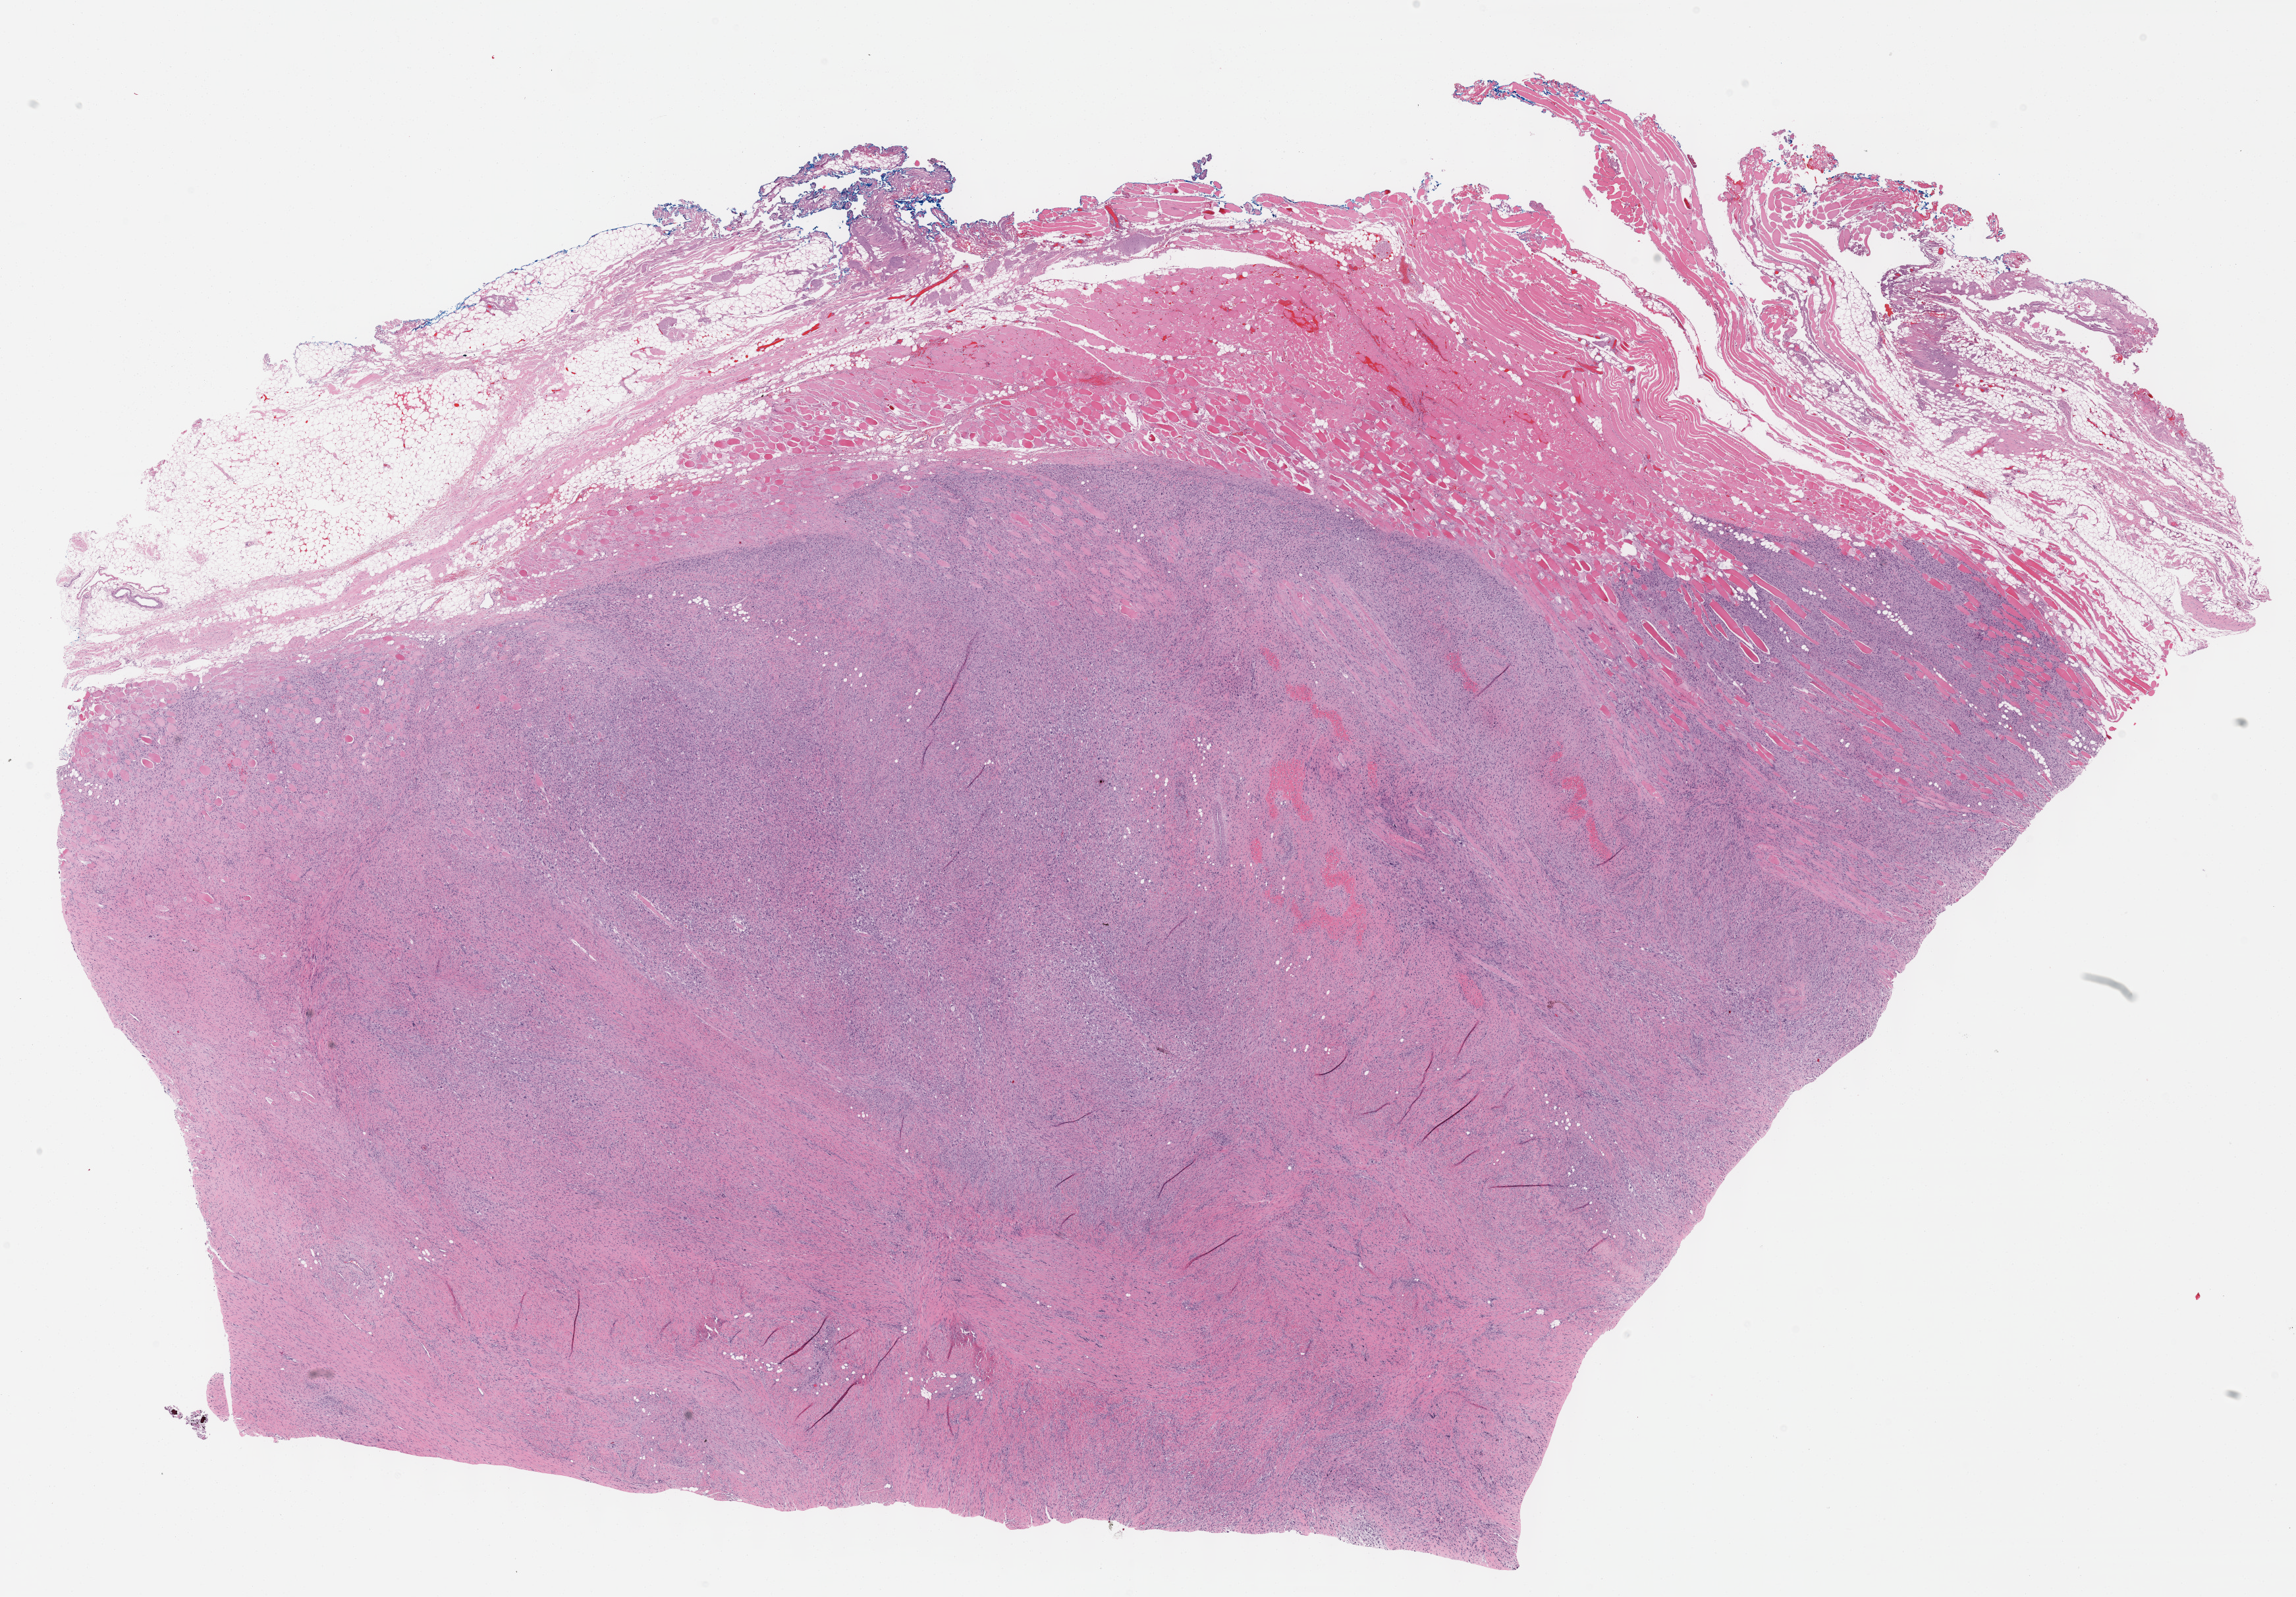
Digitized H&E tissue section (whole slide), low-resolution overview of the scanned area, about 28.2 x 19.6 mm. Formalin-fixed paraffin-embedded (FFPE) diagnostic section. Sample: primary tumour, connective, subcutaneous and other soft tissues. Male patient; age at initial diagnosis 76 years.
Diagnosis: Malignant fibrous histiocytoma (connective, subcutaneous and other soft tissues of thorax).